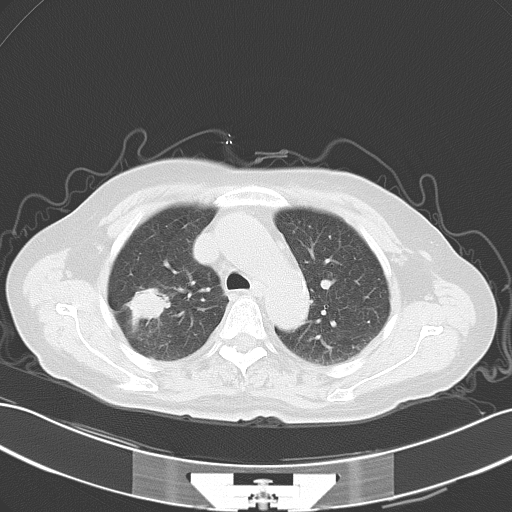
Chest CT, one axial slice. Position 42 of 57 along the scan axis. Reconstruction kernel B70f. 120 kVp. Lung window (W 1500 / L -600 HU). 5 mm slice thickness. 512 × 512 image matrix, field of view 353 × 353 mm. Female patient, age 65 years. Case-level facts recorded for this patient, not image findings: clinical TNM (as recorded): T1c N0 M1c.
Structures marked on this image (bounding box drawn by a radiologist):
- lung tumour (recorded histology: adenocarcinoma): bounding box [x1, y1, x2, y2] px = [125, 284, 173, 330]